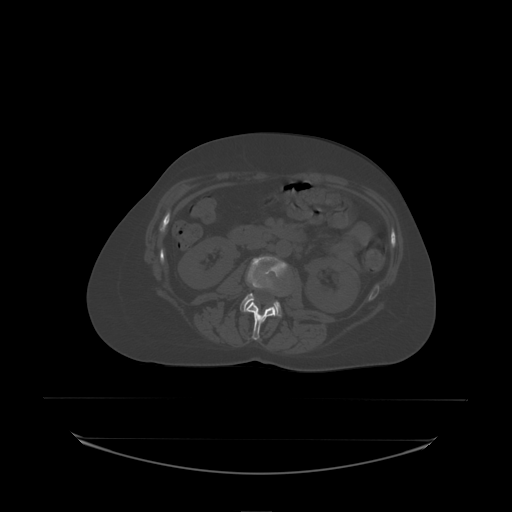
CT including the spine, one axial slice. Slice 67 of 242 in the series (ordered by position). Bone window (W 1800 / L 400 HU). 2.5 mm slice thickness. 512 × 512 image matrix. Patient: female, 53 years. Case-level facts recorded for this patient, not image findings: primary cancer: lung.
Structures marked on this image (semi-automatically segmented with operator editing):
- L2 vertebra: box from (x=245, y=301) to (x=279, y=338) px
- L3 vertebra: (x=240, y=256)–(x=288, y=317)